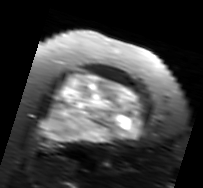
MRI of an extremity soft-tissue mass, one axial slice. Slice 56 of 91 in the series (ordered by position). T2-weighted fat-saturated. MR volume resampled by the dataset authors to the PET/CT grid (not the native acquisition matrix). 203 × 188 image matrix, field of view 198 × 184 mm. Female patient. Case-level facts recorded for this patient, not image findings: histological type: malignant solitary fibrous tumor; grade: intermediate; site of the primary tumour: right thigh.
Annotated regions visible in this slice (expert contour drawn on MRI and transferred to this co-registered scan by the dataset authors):
- gross tumour volume including surrounding oedema: bounding box (x1, y1, x2, y2) in pixels: (40, 70, 148, 146)
- gross tumour volume (mass): (40, 72, 144, 146)